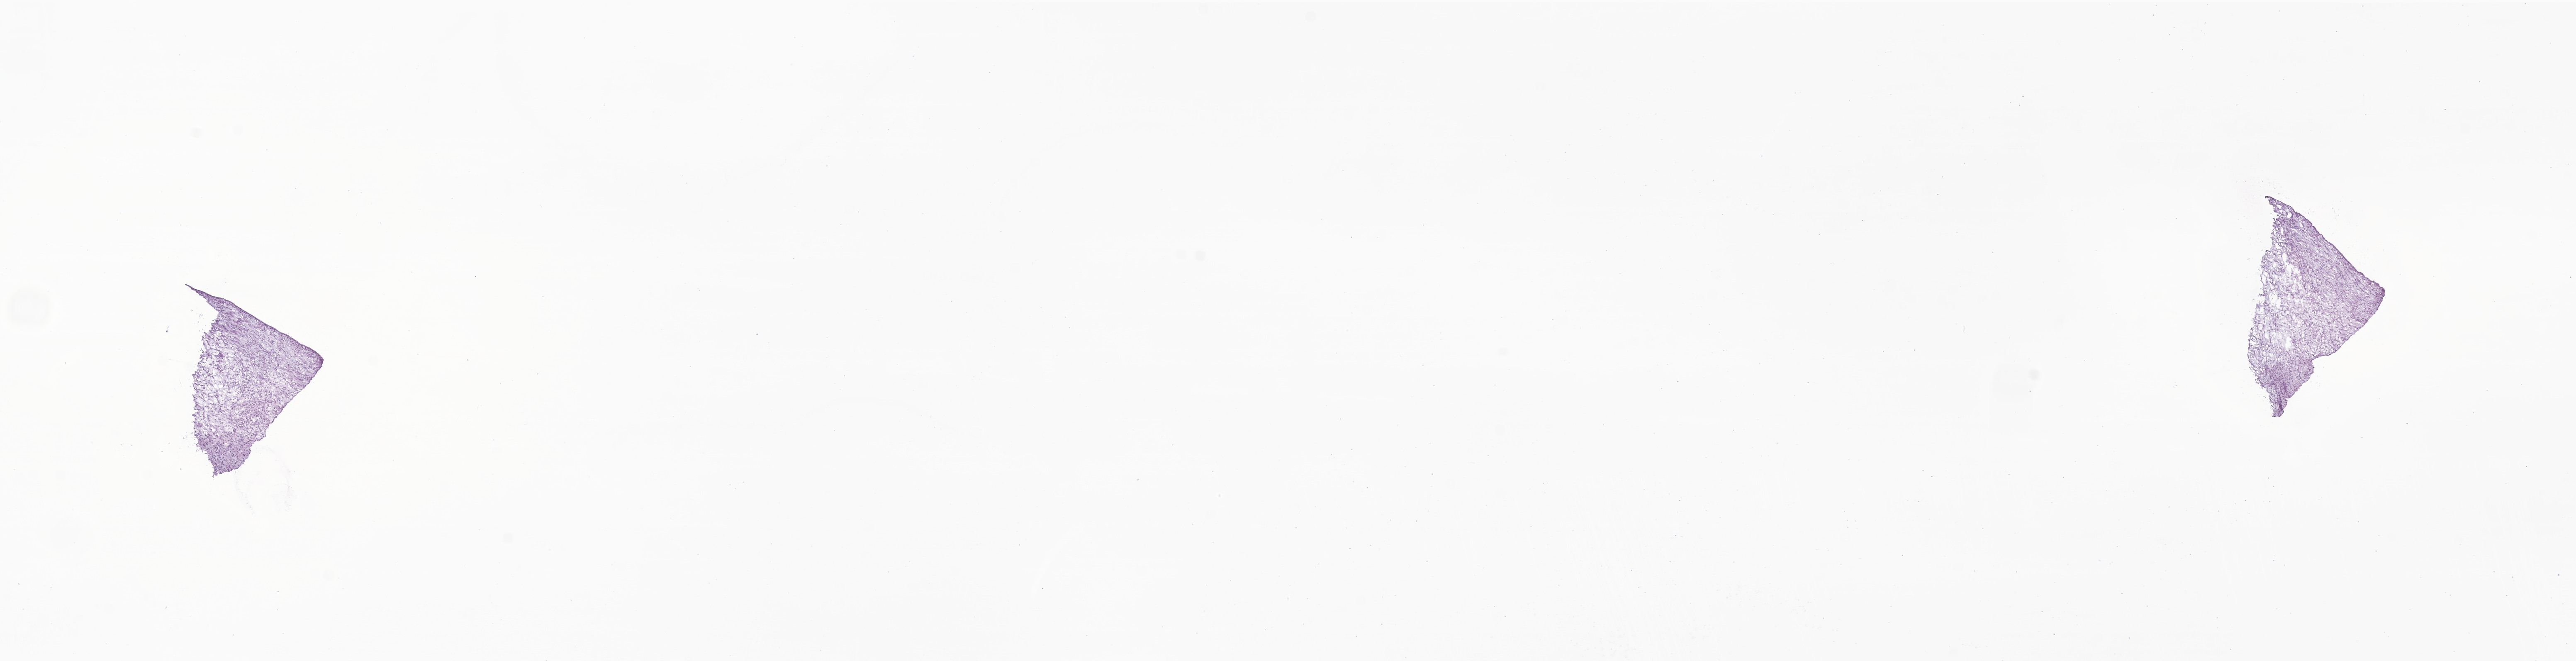
Digitized H&E-stained section of tumor tissue from the soft tissue, a low-resolution overview of the entire scanned area, about 26.2 x 6.7 mm; cryosection (OCT / tissue freezing medium). Patient female; age 216 days.
* diagnosis: Myofibroblastic tumor, NOS